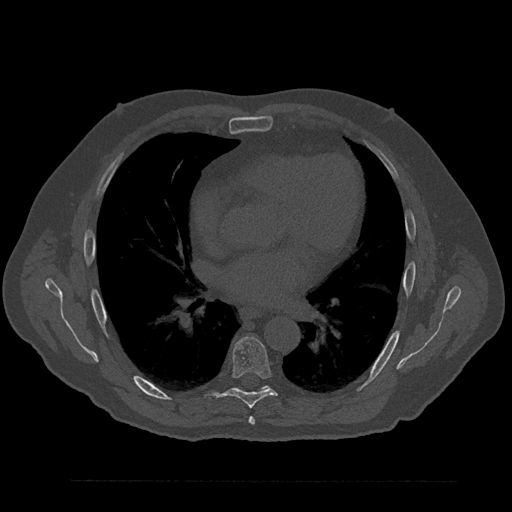
CT including the spine, one axial slice; position 502 of 797 along the scan axis; reconstruction kernel Br40s/3; bone window (W 1800 / L 400 HU); 0.5 mm slice thickness; 512 × 512 image matrix. Patient: male, 61 years. Case-level facts recorded for this patient, not image findings: primary cancer: prostate.
Structures marked on this image (semi-automatically segmented with operator editing):
- T6 vertebra: box from (x=249, y=416) to (x=255, y=425) px
- T7 vertebra: (x=208, y=337)–(x=277, y=408)
- T8 vertebra: (x=262, y=386)–(x=268, y=389)